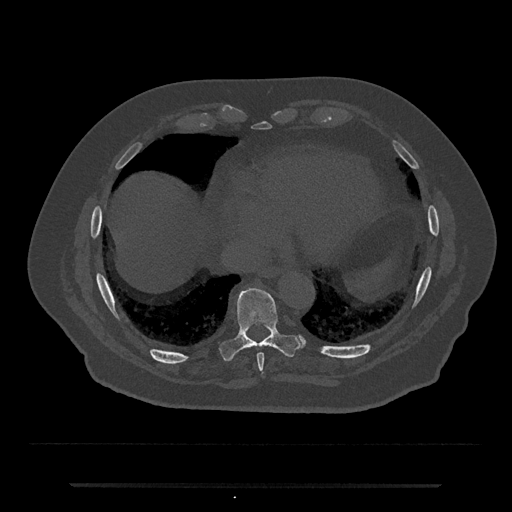
CT including the spine, one axial slice. 120 kVp. Bone window (W 1800 / L 400 HU). 0.5 mm slice thickness. 512 × 512 image matrix, field of view 434 × 434 mm. Patient: male, 80 years. From the clinical record (not read from this slice): primary cancer: prostate.
Structures marked on this image (semi-automatically segmented with operator editing):
- T8 vertebra: bounding box [x1, y1, x2, y2] px = [257, 353, 264, 376]
- T9 vertebra: [221, 286, 303, 361]